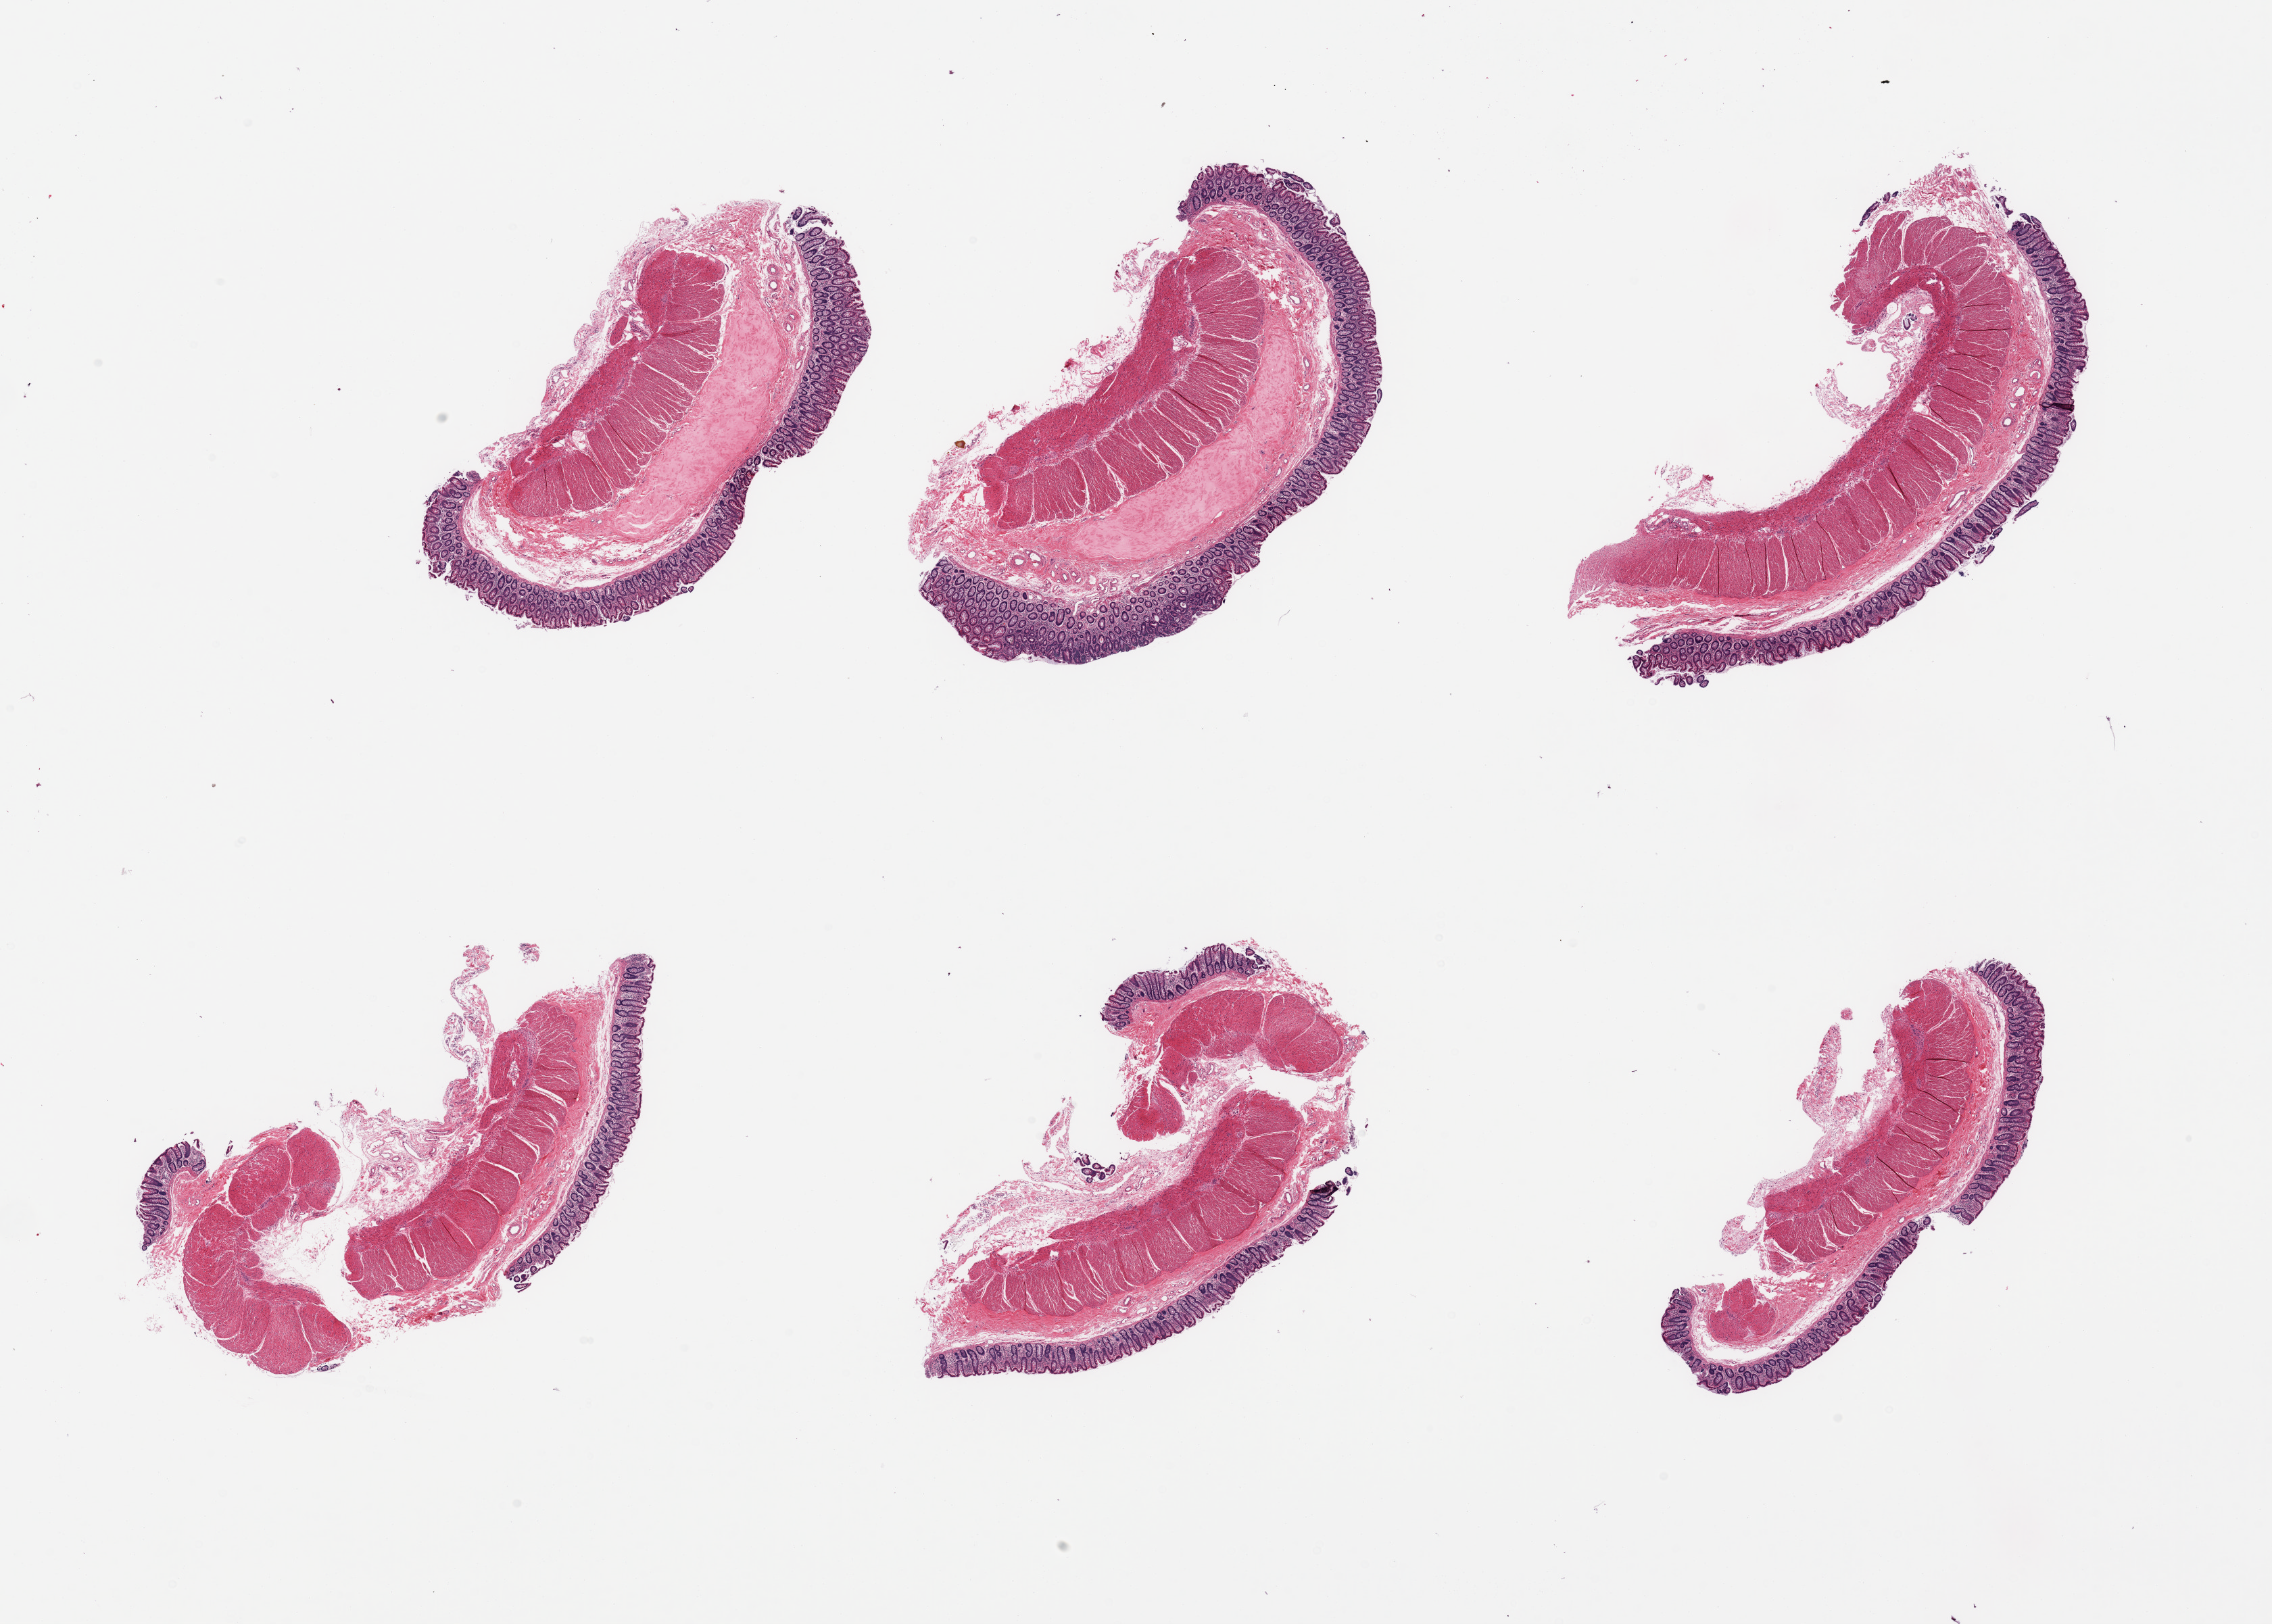
H&E whole-slide image — a low-resolution overview of the entire scanned area, about 26.6 x 19.0 mm (from a 20x scan), PAXgene-fixed paraffin-embedded (PFPE) section, target tissue: transverse colon, tissue donor sample. Donor sex: male.
Review note (as recorded): 6 pieces; foci of edematous, amyloid-like stroma or fibroelastosis in submucosa of 2 pieces, measuring up to 3x1mm, like in sigmoid colon; no sign of amyloid in other tissues.